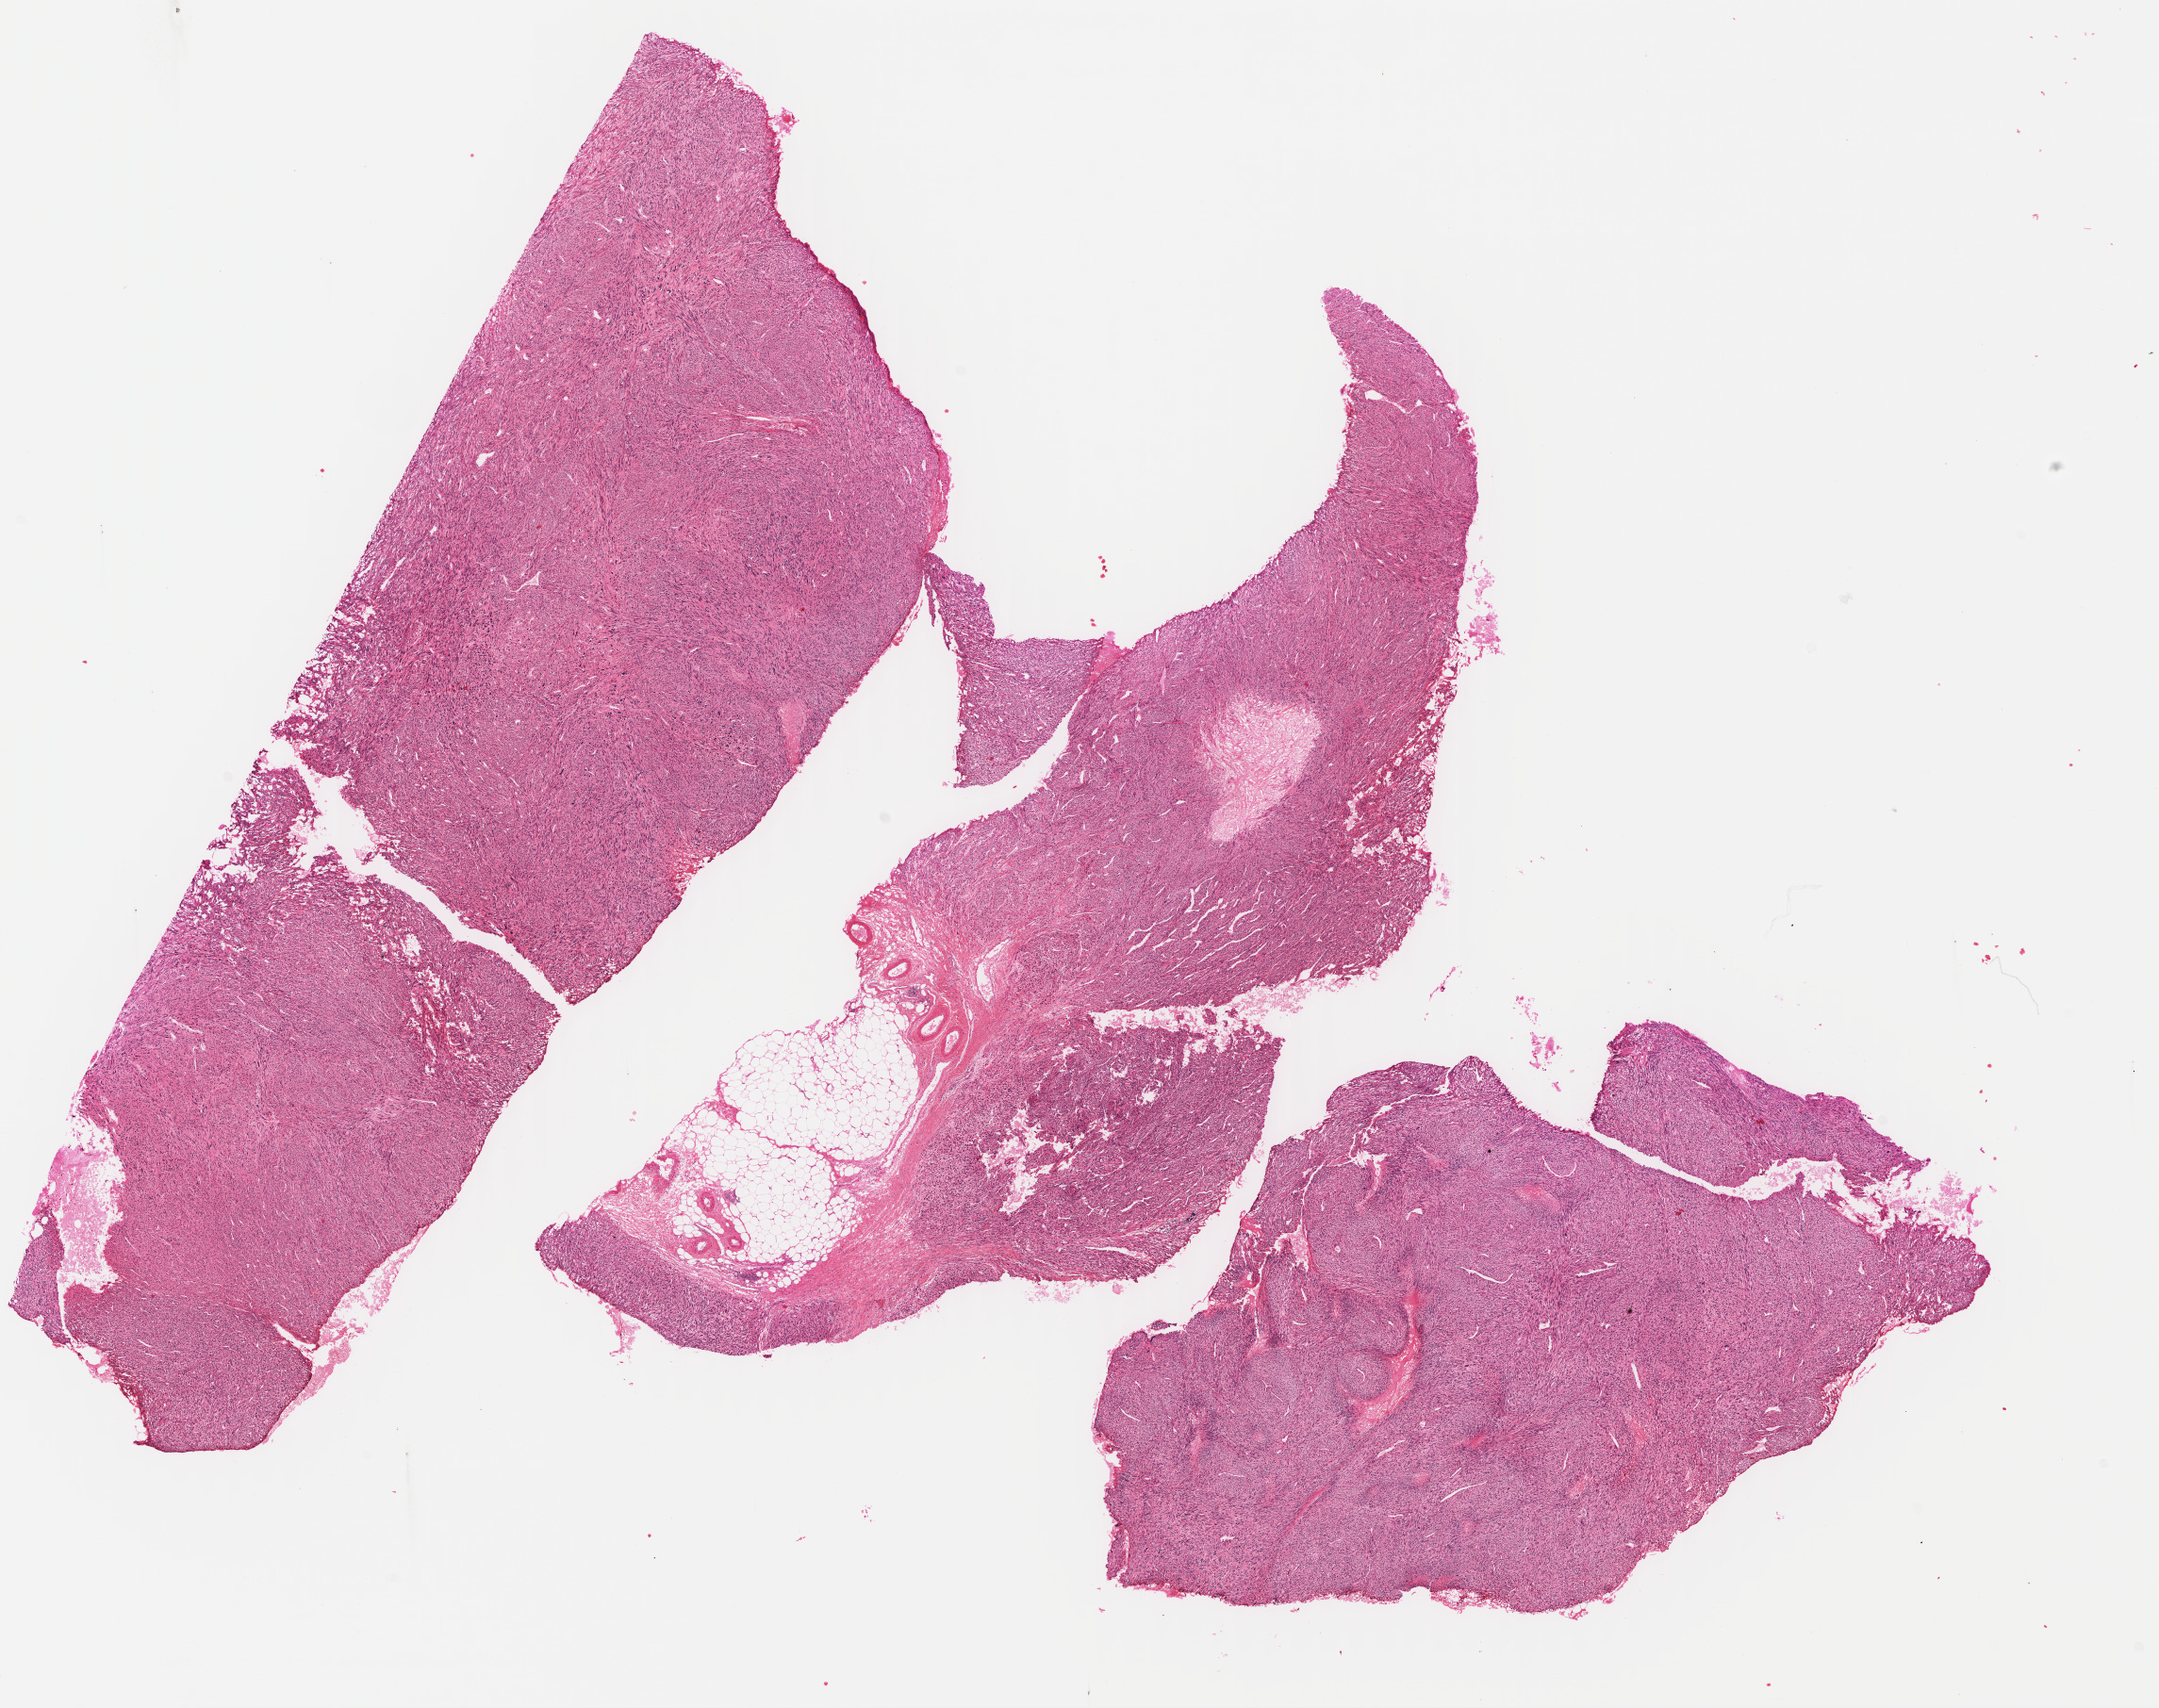
Whole-slide histology image, H&E-stained, low-resolution overview of the scanned area, about 18.0 x 14.2 mm (acquisition: 40x scan); formalin-fixed paraffin-embedded (FFPE) diagnostic section; retroperitoneum and peritoneum, primary tumour sample. Patient: female, age at initial diagnosis 59 years.
• histologic diagnosis: Leiomyosarcoma, NOS (retroperitoneum)